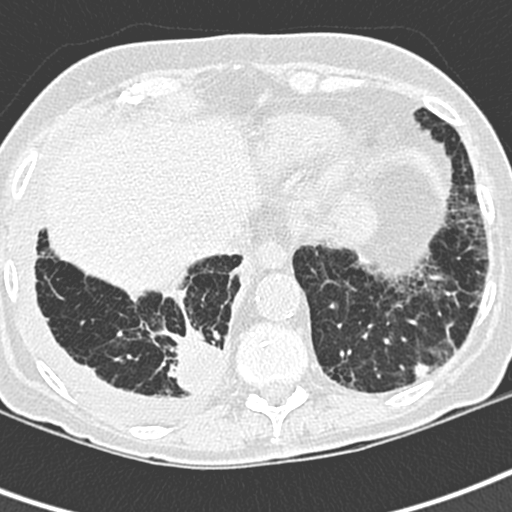
Low-dose screening chest CT, one axial slice; position 68 of 220 along the scan axis; lung window (W 1500 / L -600 HU); 512 × 512 image matrix, field of view 288 × 288 mm.
Structures marked on this image (outlined manually by an expert reader):
- lesion 1 (tumor, lower lobe of right lung): box from (x=168, y=327) to (x=221, y=394) px
- lesion 2 (nodule, lower lobe of left lung): (x=414, y=363)–(x=431, y=377)